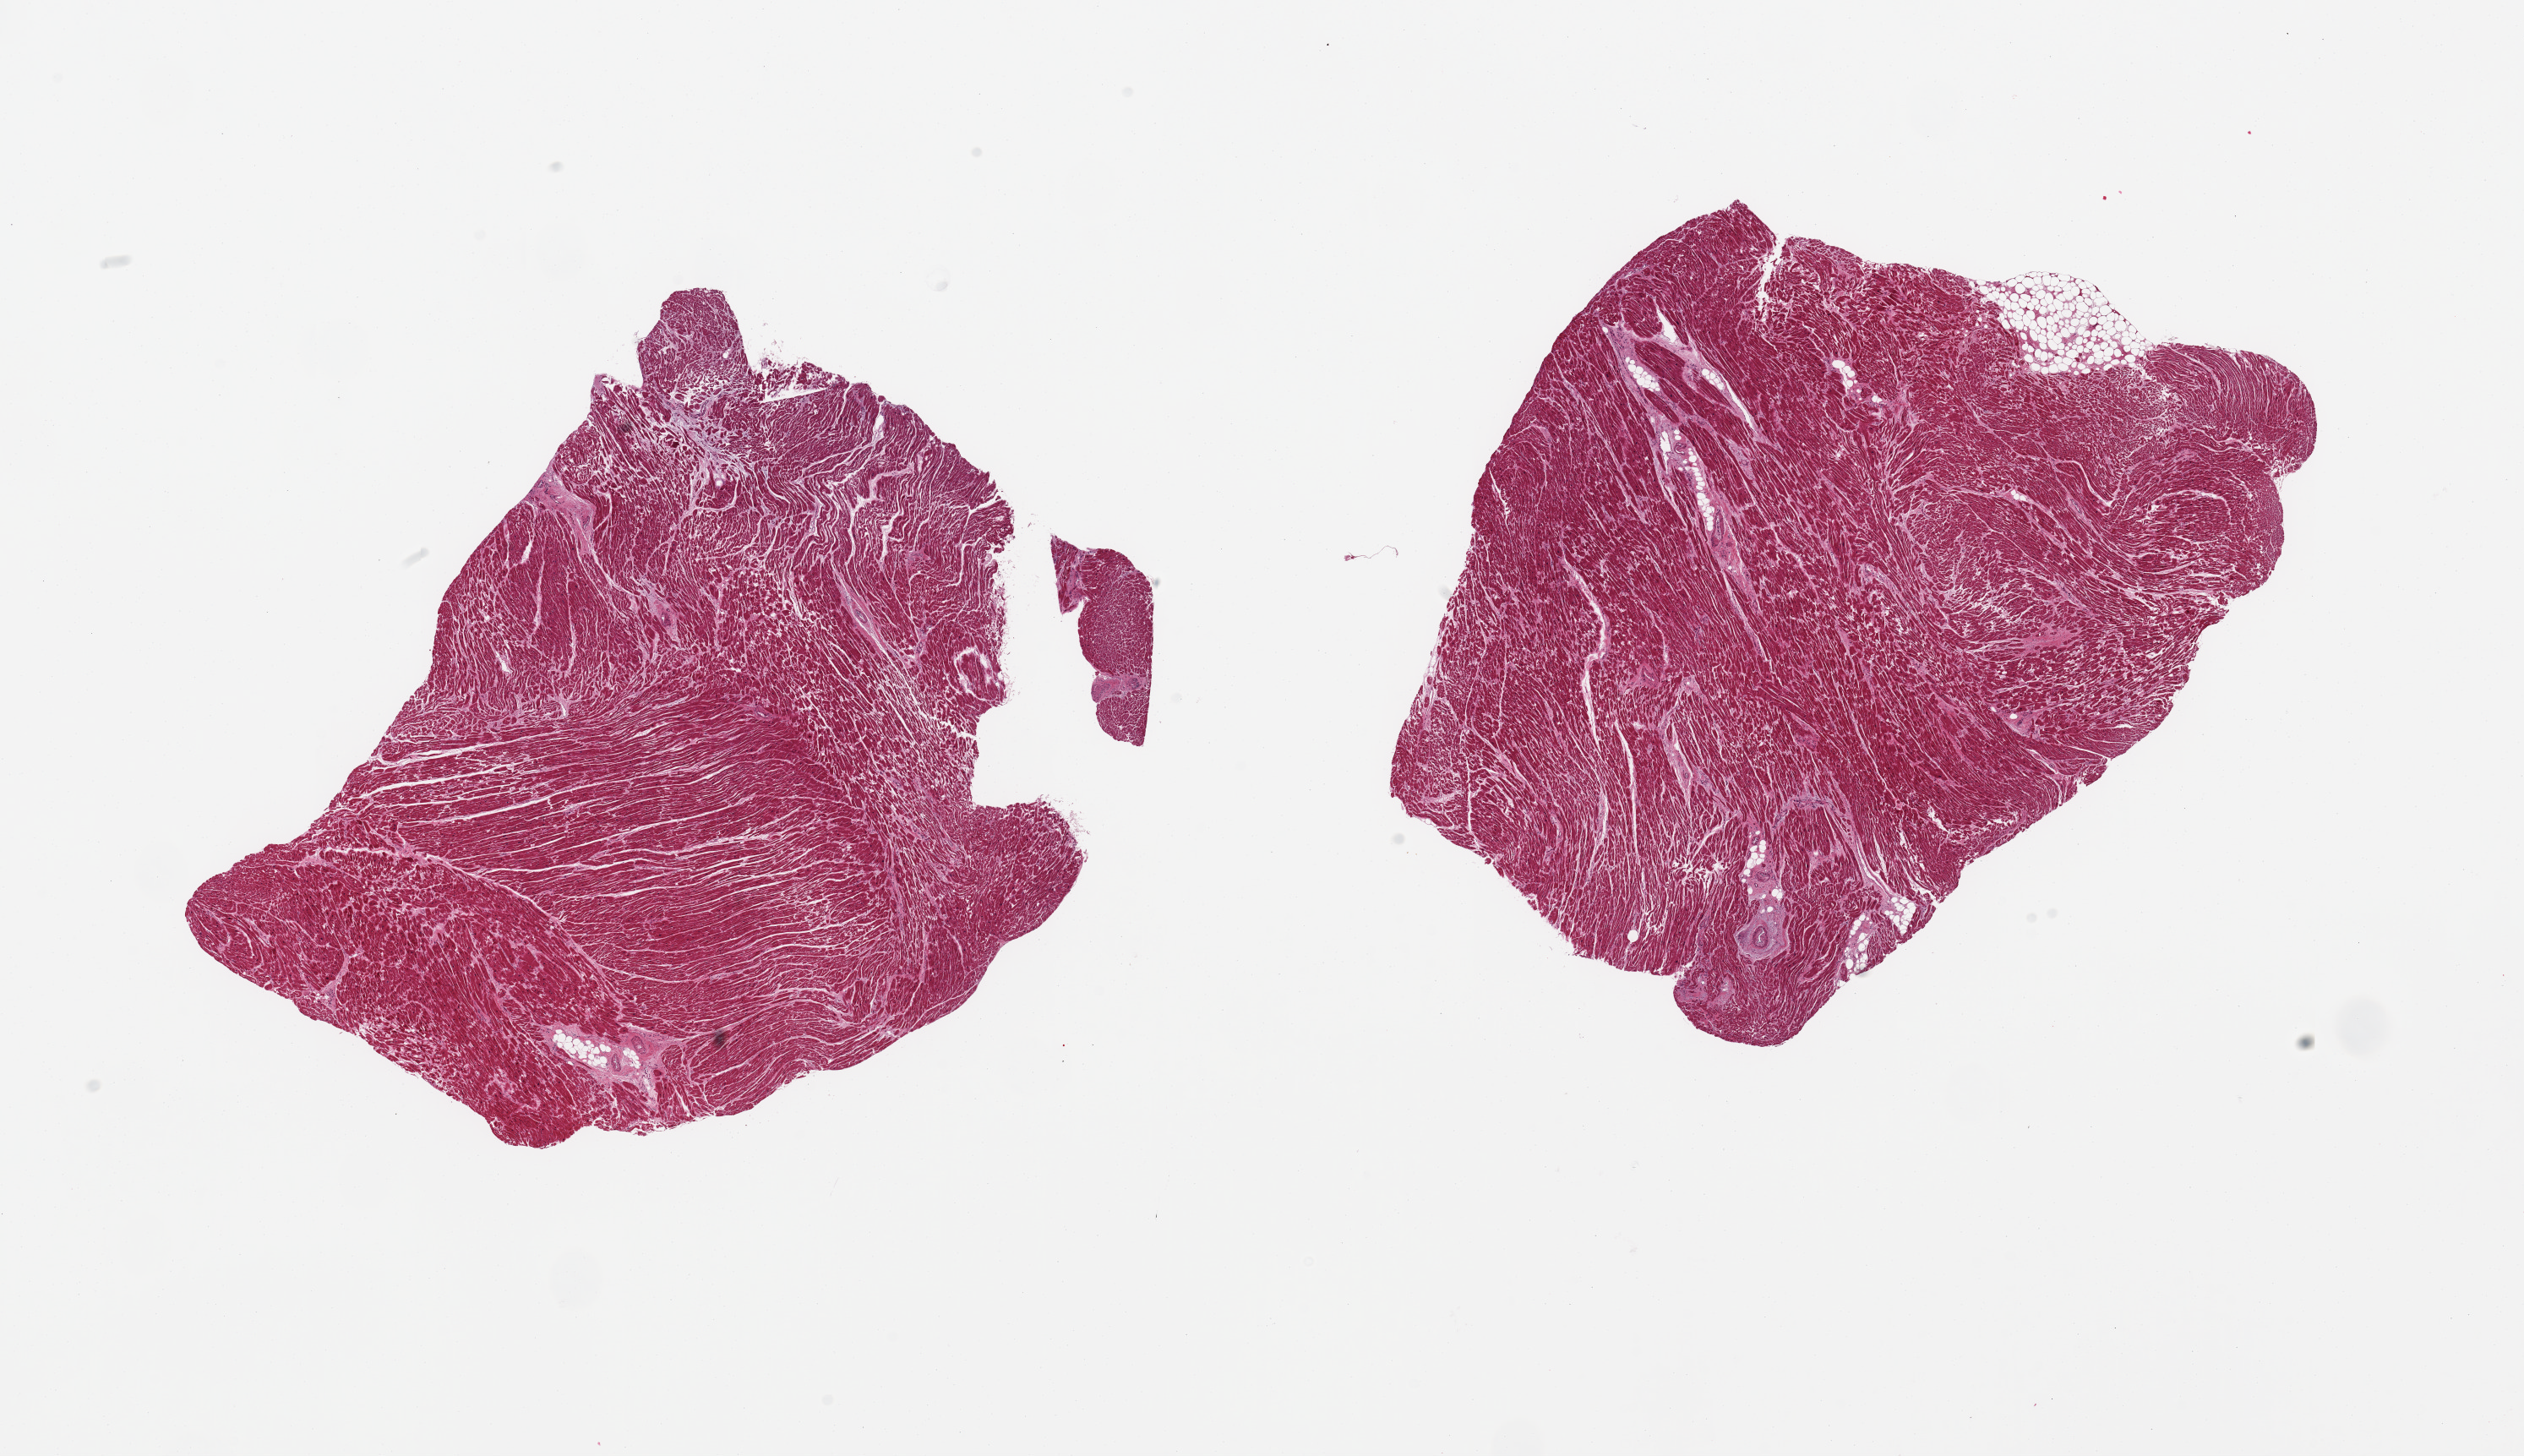
Whole-slide image, hematoxylin and eosin (H&E) stain, a low-resolution overview of the entire scanned area, about 23.6 x 13.6 mm. PAXgene-fixed, paraffin-embedded tissue. Sampled site (target tissue): heart. Donor tissue sample. Male donor.
Review note (as recorded): 2 pieces; interstitial fibrosis with ? ischemic changes.